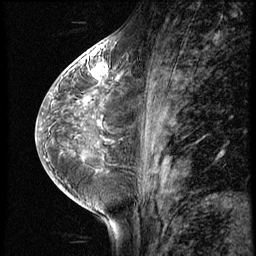
Breast MRI (dynamic contrast-enhanced), one sagittal slice; position 28 of 56 along the scan axis; 3 images stored at this slice position (order not interpretable as contrast timing); 1.5 T; TE 4.2 ms, TR 8.9 ms; 256 × 256 image matrix, field of view 200 × 200 mm. Patient: female, 38 years. Case-level facts recorded for this patient, not image findings: setting: breast cancer imaged before/during neoadjuvant chemotherapy; receptor status: triple-negative.
Structures marked on this image (semi-automatically segmented with operator editing):
- analysis volume of interest (the breast-tissue region the enhancement analysis was run in; not a lesion): bounding box [x1, y1, x2, y2] px = [88, 60, 110, 84]
- tumour enhancement mask (voxels above the 140 % enhancement threshold inside the analysis volume of interest): [93, 64, 105, 75]